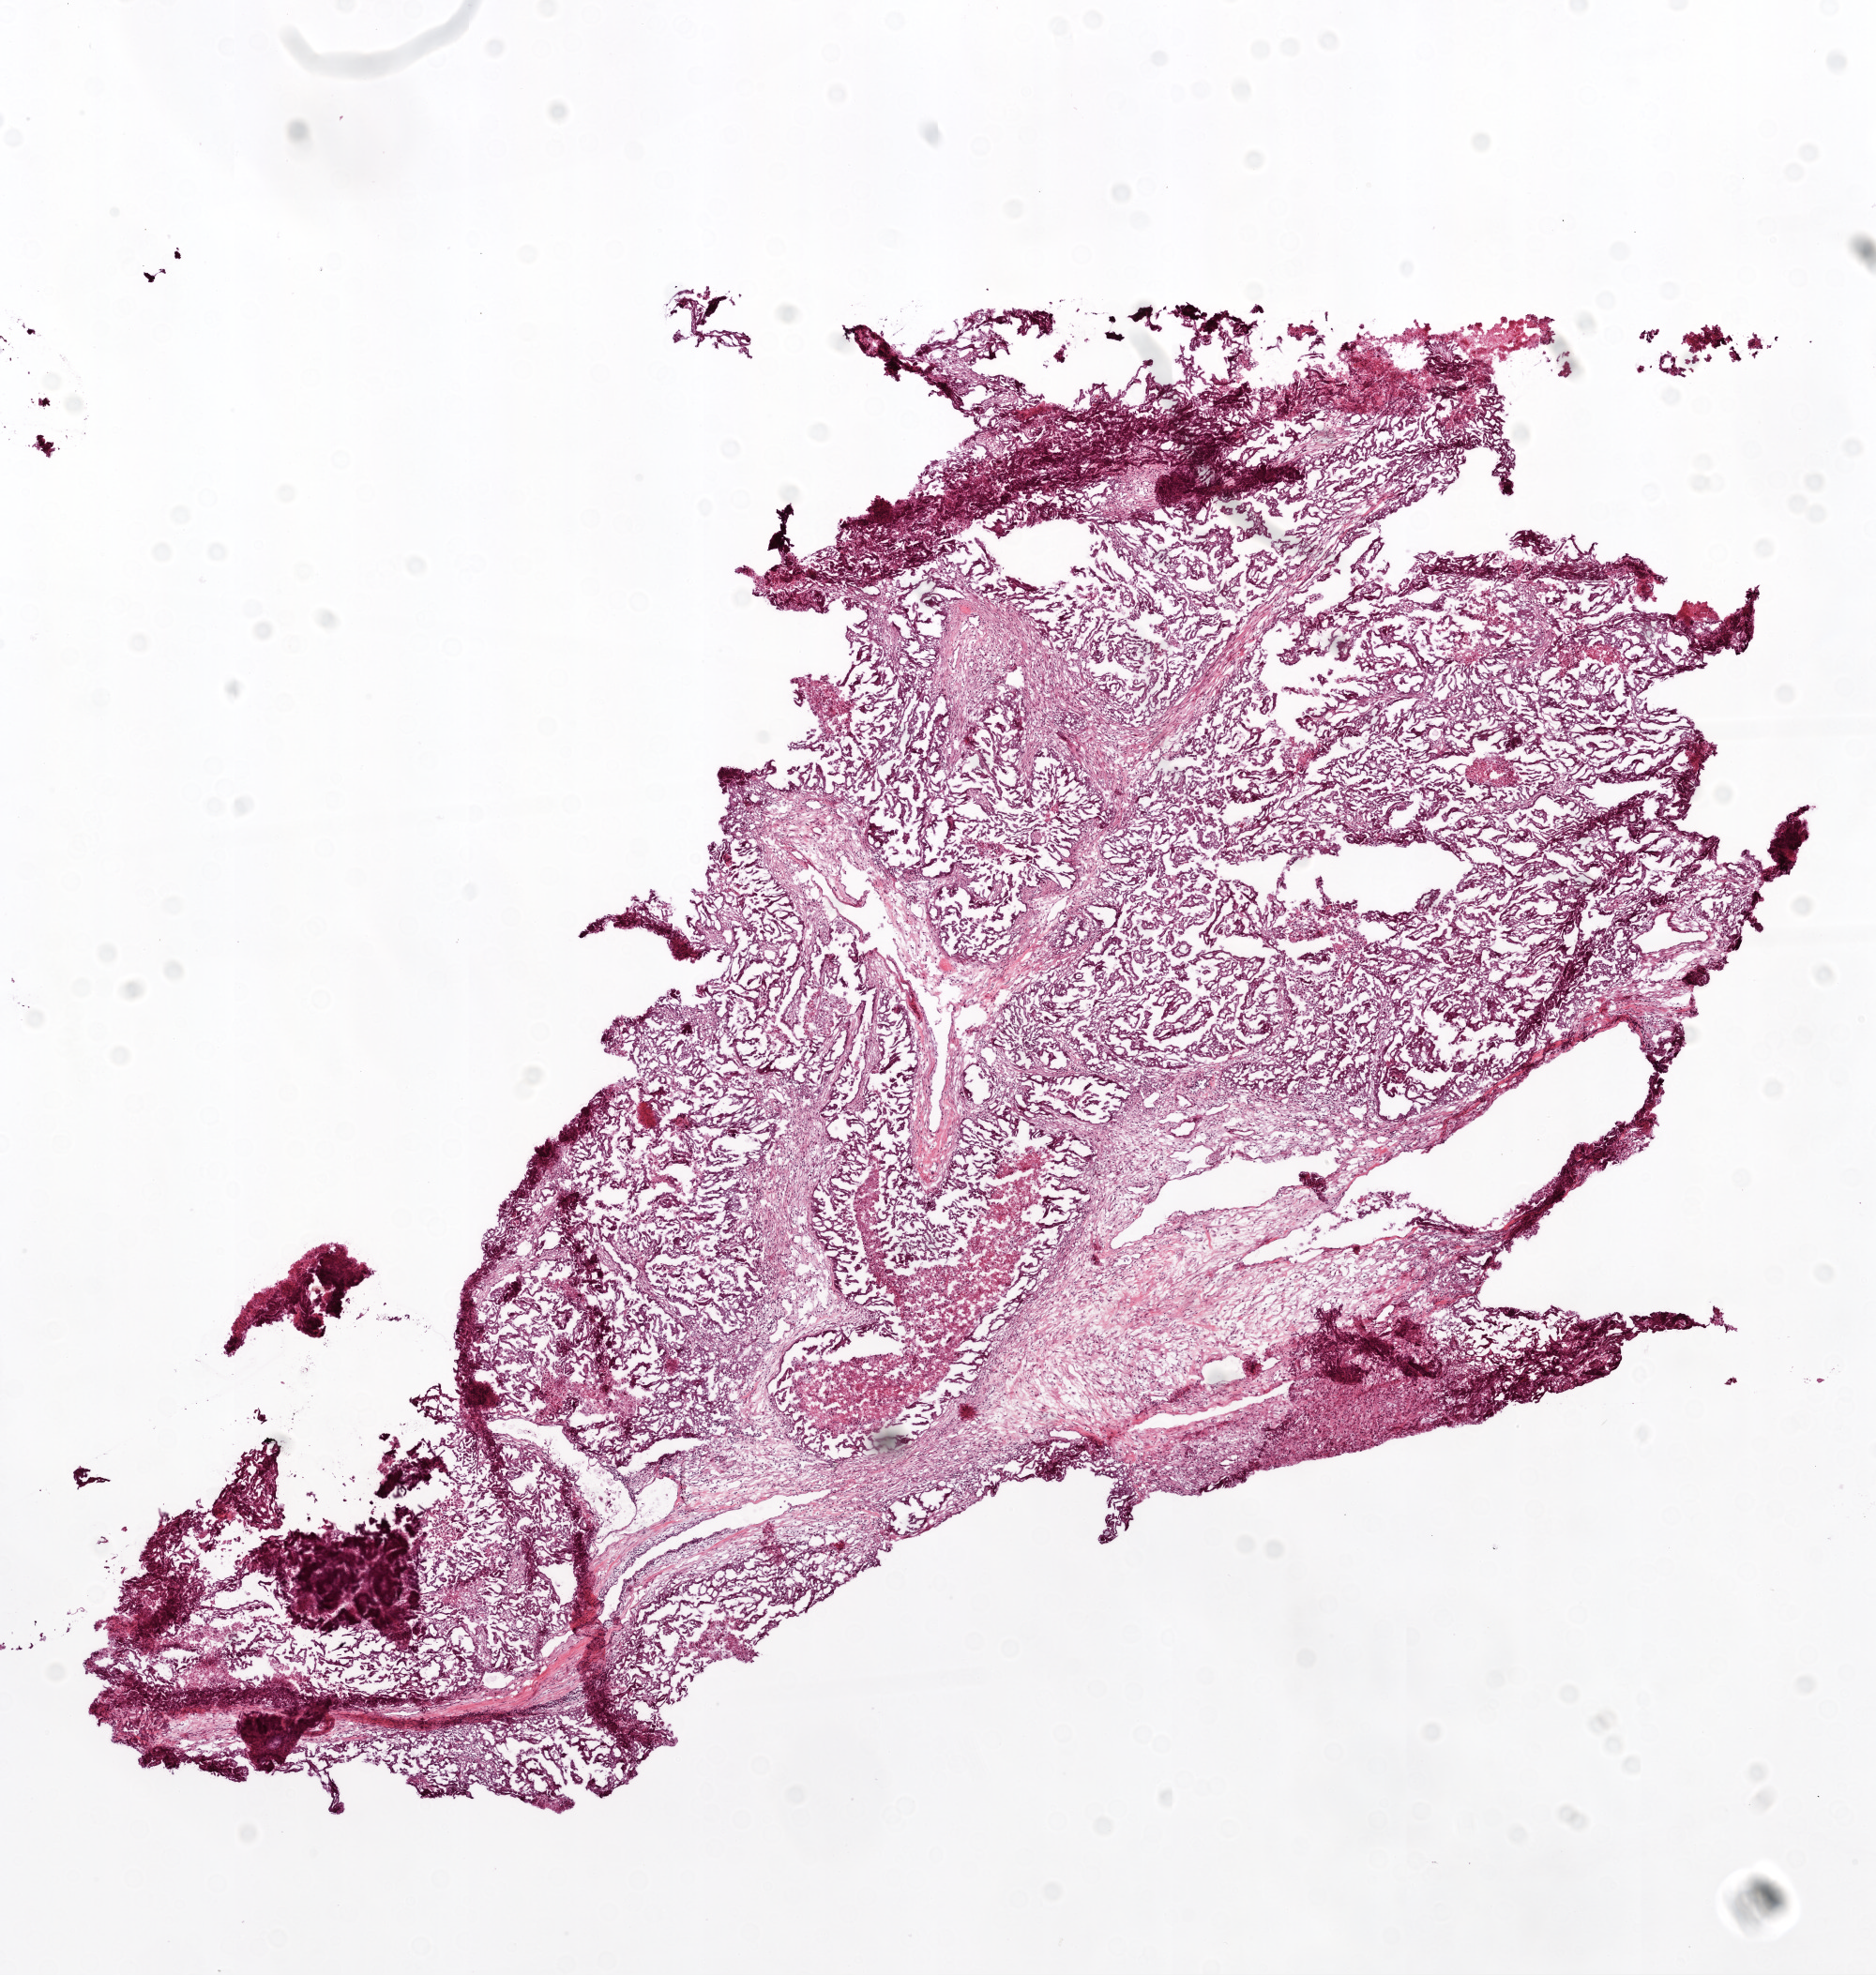
Whole-slide histology image, H&E-stained — a low-resolution overview of the entire scanned area, about 8.0 x 8.4 mm (slide scanned at 20x); frozen section from the top of the tissue portion; primary tumour sample from the ovary. Female patient; age at initial diagnosis 44 years. Histologic grade: G3 (poorly differentiated). Composition of this section per pathologist review: tumour cells 75%, tumour nuclei 80%, normal cells 1%, stromal cells 19%, necrosis 5%.
FIGO stage: IV. Histologic diagnosis: Serous cystadenocarcinoma, NOS. Laterality: bilateral.